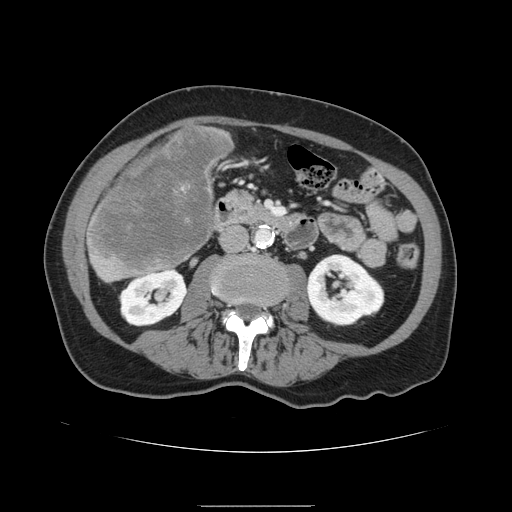
Contrast-enhanced abdominal CT, one axial slice; position 41 of 168 along the scan axis; 120 kVp; intravenous contrast given; soft-tissue window (W 400 / L 40 HU); 512 × 512 image matrix, field of view 386 × 386 mm. Male patient, age 74 years. Case-level facts recorded for this patient, not image findings: diagnosis: colorectal cancer liver metastases, imaged before liver resection; multiple liver metastases: no; largest metastasis: 14.5 cm; chemotherapy before resection: no.
Outlined on this slice (outlined manually by an expert reader):
- liver: box from (x=86, y=126) to (x=233, y=282) px
- liver metastasis: (x=88, y=128)–(x=231, y=272)